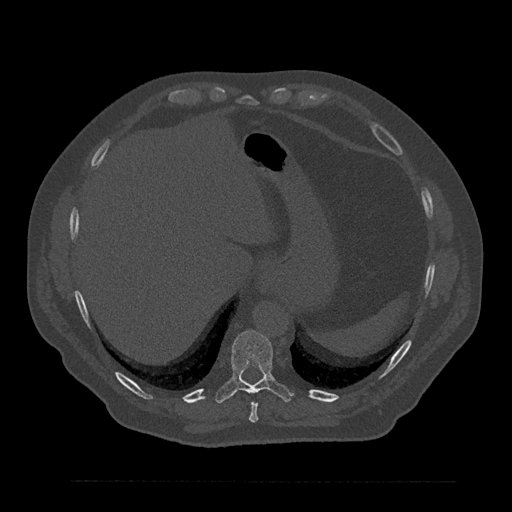
CT including the spine, one axial slice. Slice 359 of 797 in the series (ordered by position). 120 kVp. Bone window (W 1800 / L 400 HU). 0.5 mm slice thickness. 512 × 512 image matrix. Male patient, age 61 years. Case-level facts recorded for this patient, not image findings: primary cancer: prostate.
Annotated regions visible in this slice (semi-automatic segmentation, software-assisted and operator-edited):
- T10 vertebra: bounding box <215,330,293,403> (left, top, right, bottom; pixels)
- T9 vertebra: <249,402,258,423>